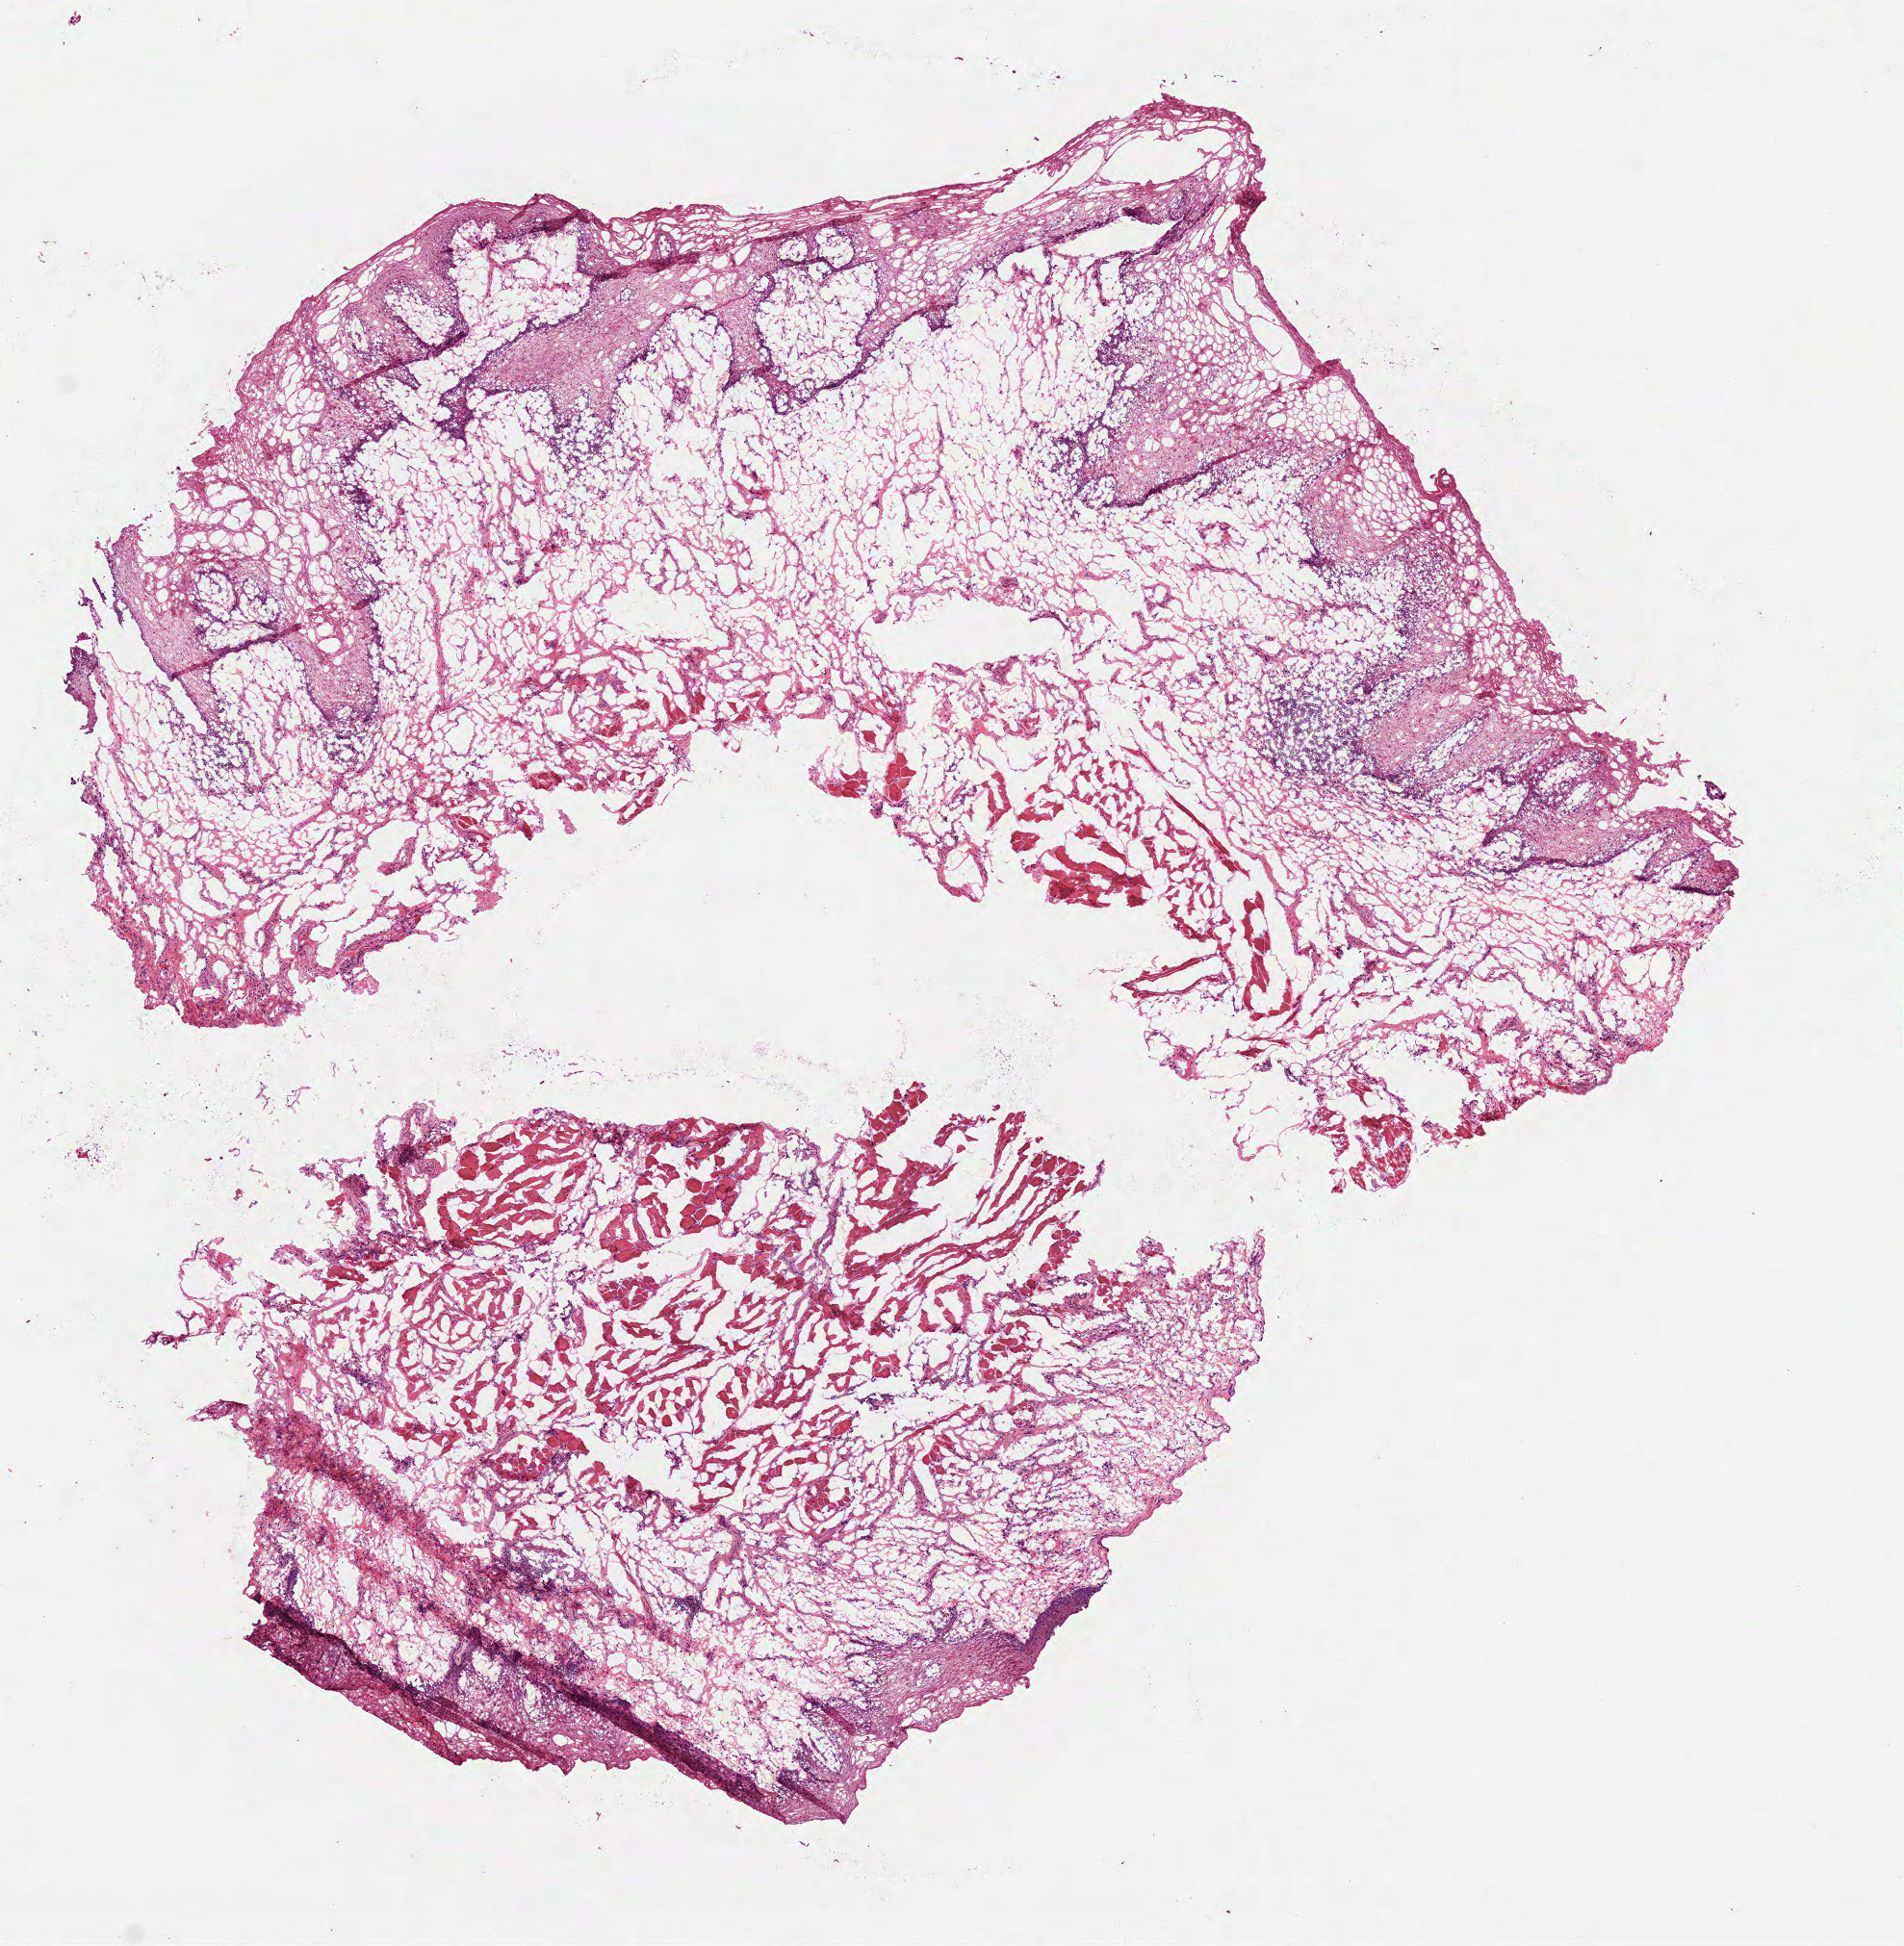
H&E-stained whole-slide image — shown as a low-resolution overview of the whole scanned area (about 8.0 x 8.2 mm, from a 40x scan), frozen section from the top of the tissue portion, solid tissue normal (non-tumour tissue) sample from the head and neck. Male patient; age at initial diagnosis 64 years.
This section: solid tissue normal sample (biorepository sample class). Patient diagnosis: Squamous cell carcinoma, NOS (overlapping lesion of lip, oral cavity and pharynx).